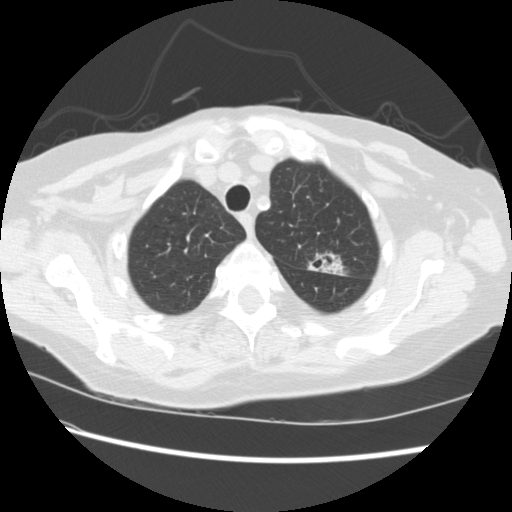
Chest CT (low-dose screening protocol), one axial image; first (baseline) screen; lung window (W 1500 / L -600 HU); 2.5 mm slice thickness; standard (soft-tissue) reconstruction kernel (STANDARD); 120 kVp; slice 43 of 224 in the series; 512 × 512 image matrix, field of view 340 × 340 mm. Female, age 74 years at enrolment. Former smoker at enrolment.
Expert reader's lesion annotation, bounding box [x1, y1, x2, y2] px = [297, 244, 347, 283]. The screening reader recorded 2 non-calcified nodules or masses ≥4 mm on this exam; which of them this box marks is not recorded. Later outcome: lung cancer diagnosed 309 days after this screen — non-small cell carcinoma, left upper lobe, stage IV (AJCC 6th edition).